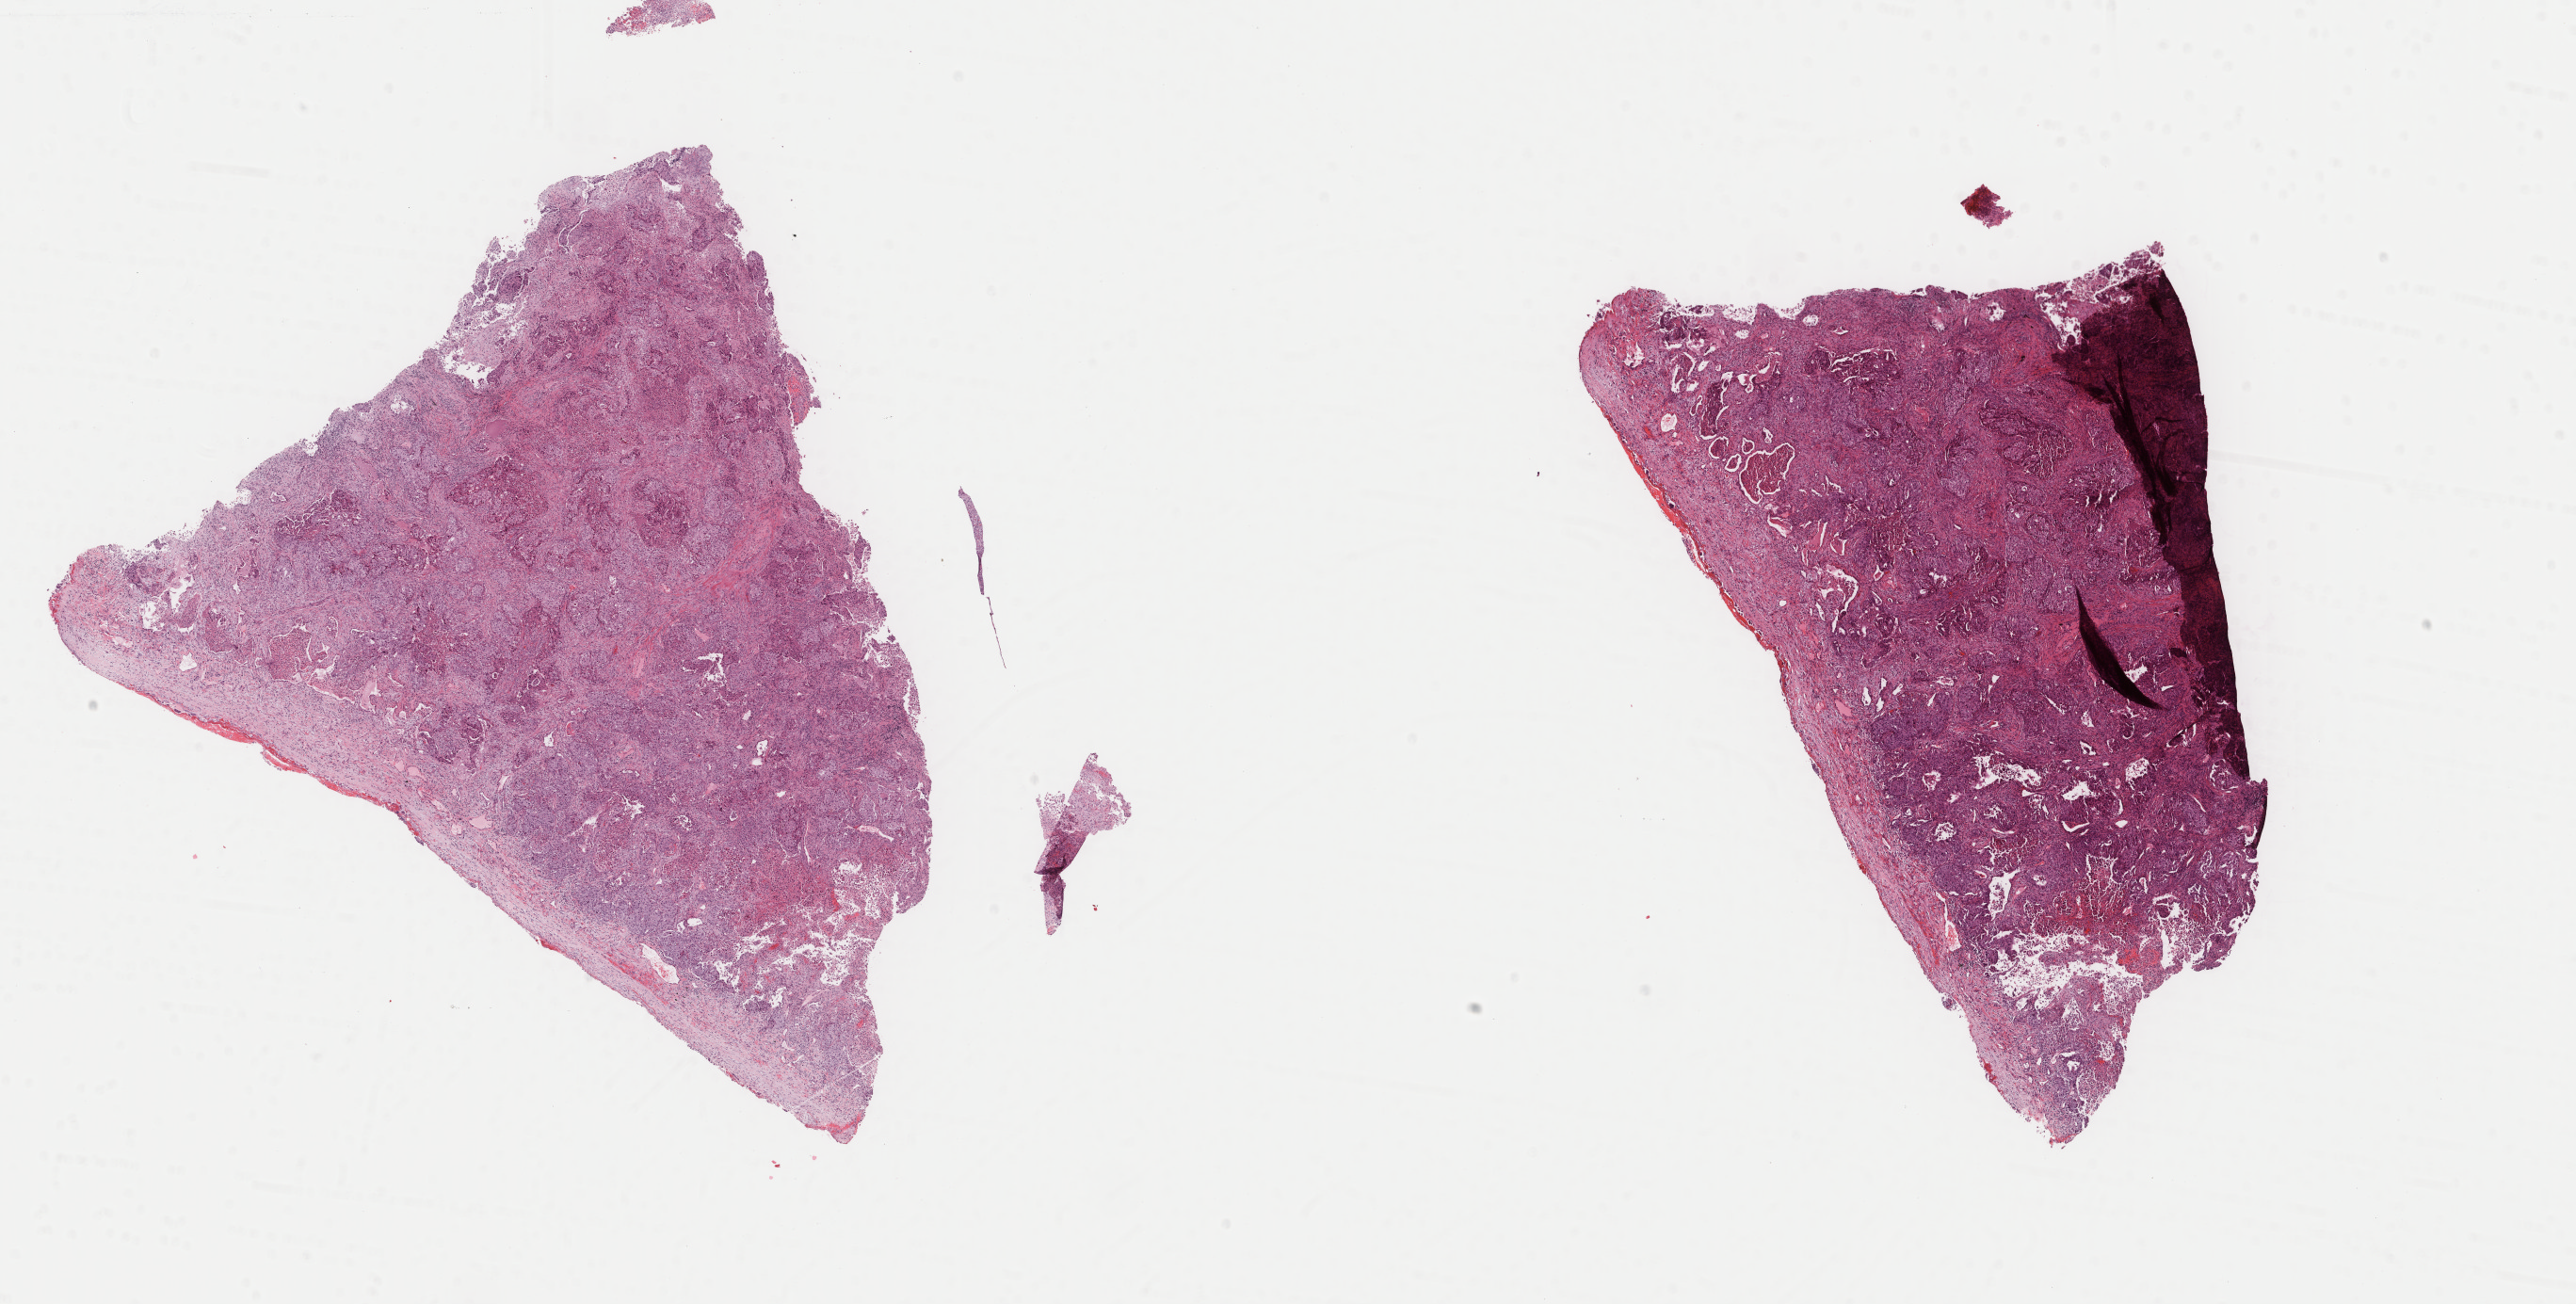
Hematoxylin and eosin (H&E) stained whole-slide image, whole scanned area (about 21.7 x 11.0 mm, acquisition: 40x scan) shown as a low-resolution overview. Frozen section from the bottom of the tissue portion. Sample: primary tumour, lung. Male, age 65 years at initial diagnosis. Slide review estimates, as recorded: tumour cells 60%, tumour nuclei 70%, normal cells 0%, stromal cells 25%, necrosis 15%. Inflammatory infiltration, as recorded: lymphocyte infiltration 50%, monocyte infiltration 50%, neutrophil infiltration 0%.
* pathologic diagnosis: Adenocarcinoma, NOS (upper lobe, lung)
* AJCC pathologic stage: IB (6th edition)